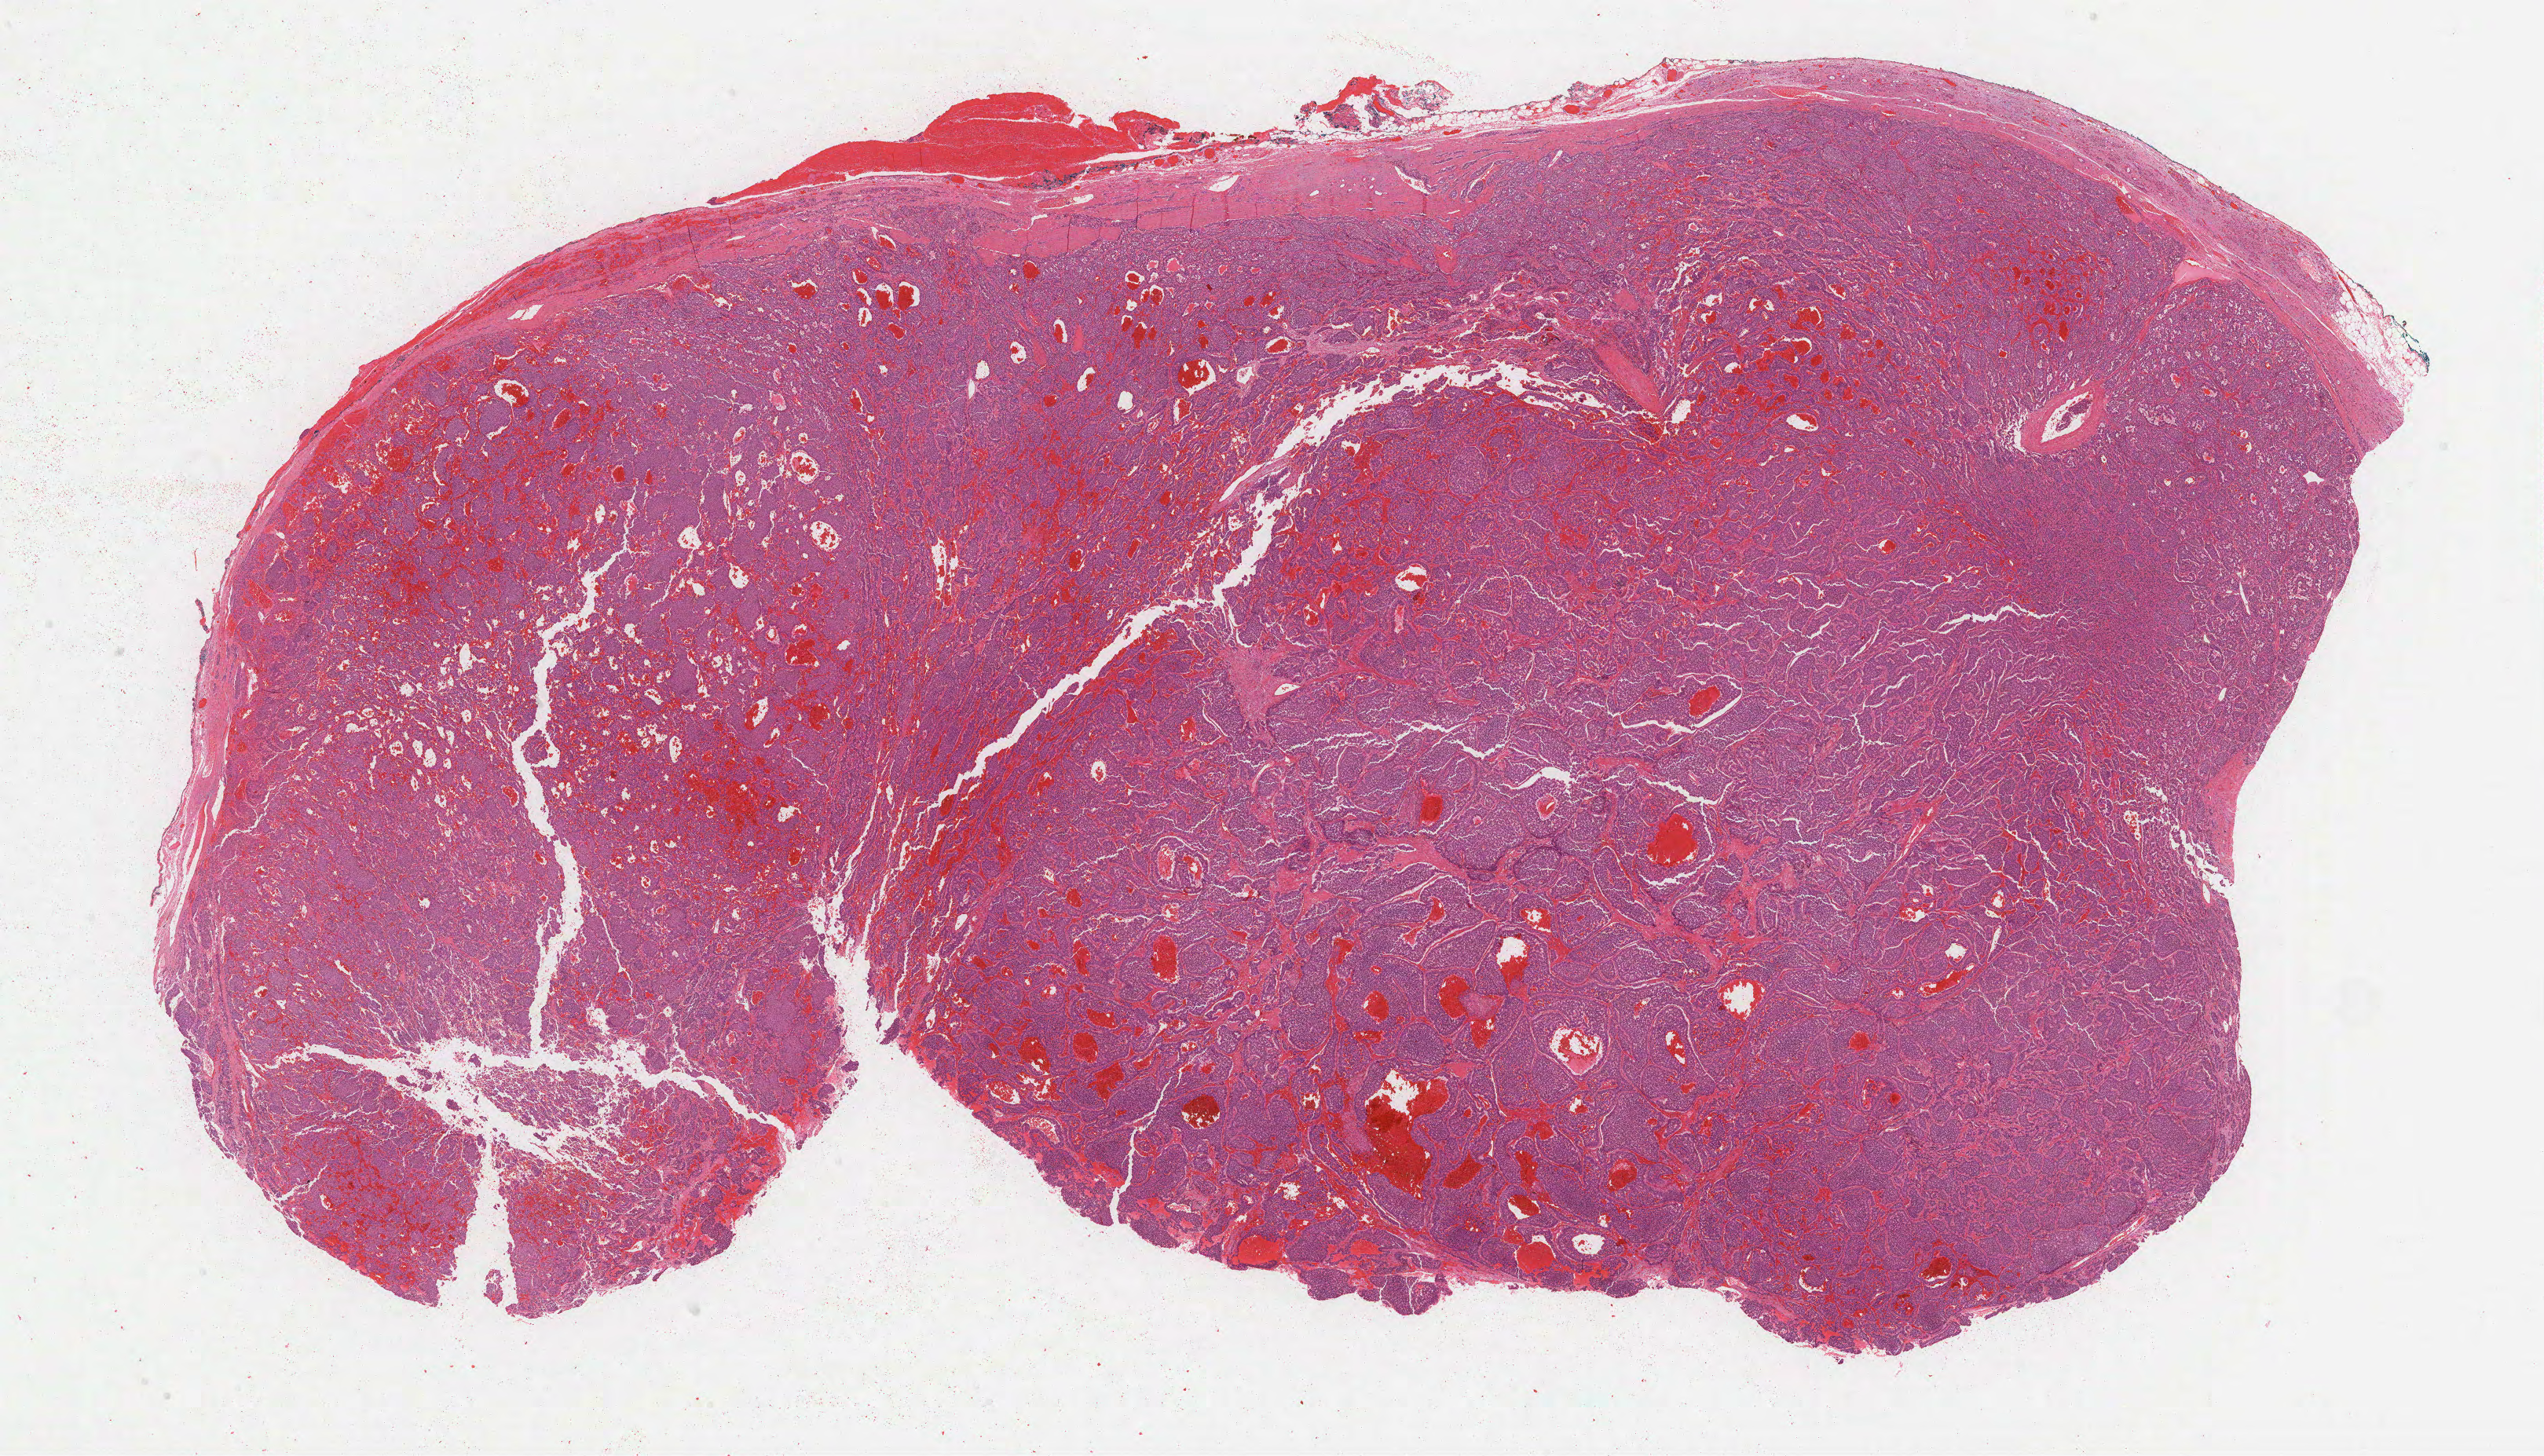
Whole-slide histology image, H&E-stained — shown as a low-resolution overview of the whole scanned area (about 26.2 x 15.0 mm, slide scanned at 40x). FFPE section. Sample: primary tumour, pancreas. Patient: female, age at initial diagnosis 64 years. Histologic grade: G1 (well differentiated).
TNM: T2 N0 MX. Lymph nodes positive (case pathology): 0 of 13 examined. Diagnosis: Neuroendocrine carcinoma, NOS. AJCC pathologic stage: IB (7th edition).